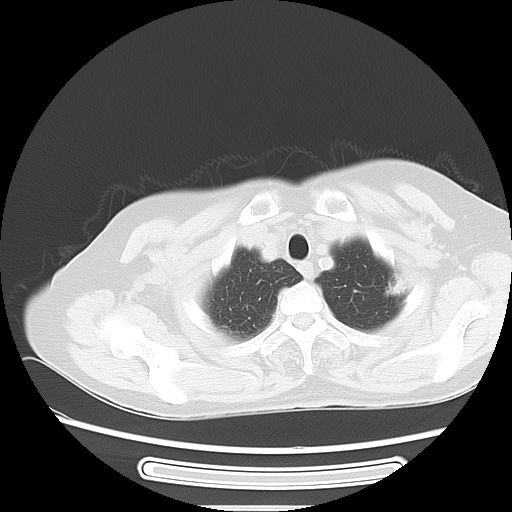
Chest CT, one axial slice; slice 43 of 52 in the series (ordered by position); reconstruction kernel LUNG; 120 kVp; lung window (W 1500 / L -600 HU); 5 mm slice thickness; 512 × 512 image matrix, field of view 350 × 350 mm. Female patient, age 57 years. Case-level facts recorded for this patient, not image findings: clinical TNM (as recorded): T1c N0 M0; histopathological grade: G2-3.
Annotated regions visible in this slice (bounding box drawn by a radiologist):
- lung tumour (recorded histology: adenocarcinoma): bounding box (x1, y1, x2, y2) in pixels: (380, 268, 411, 301)